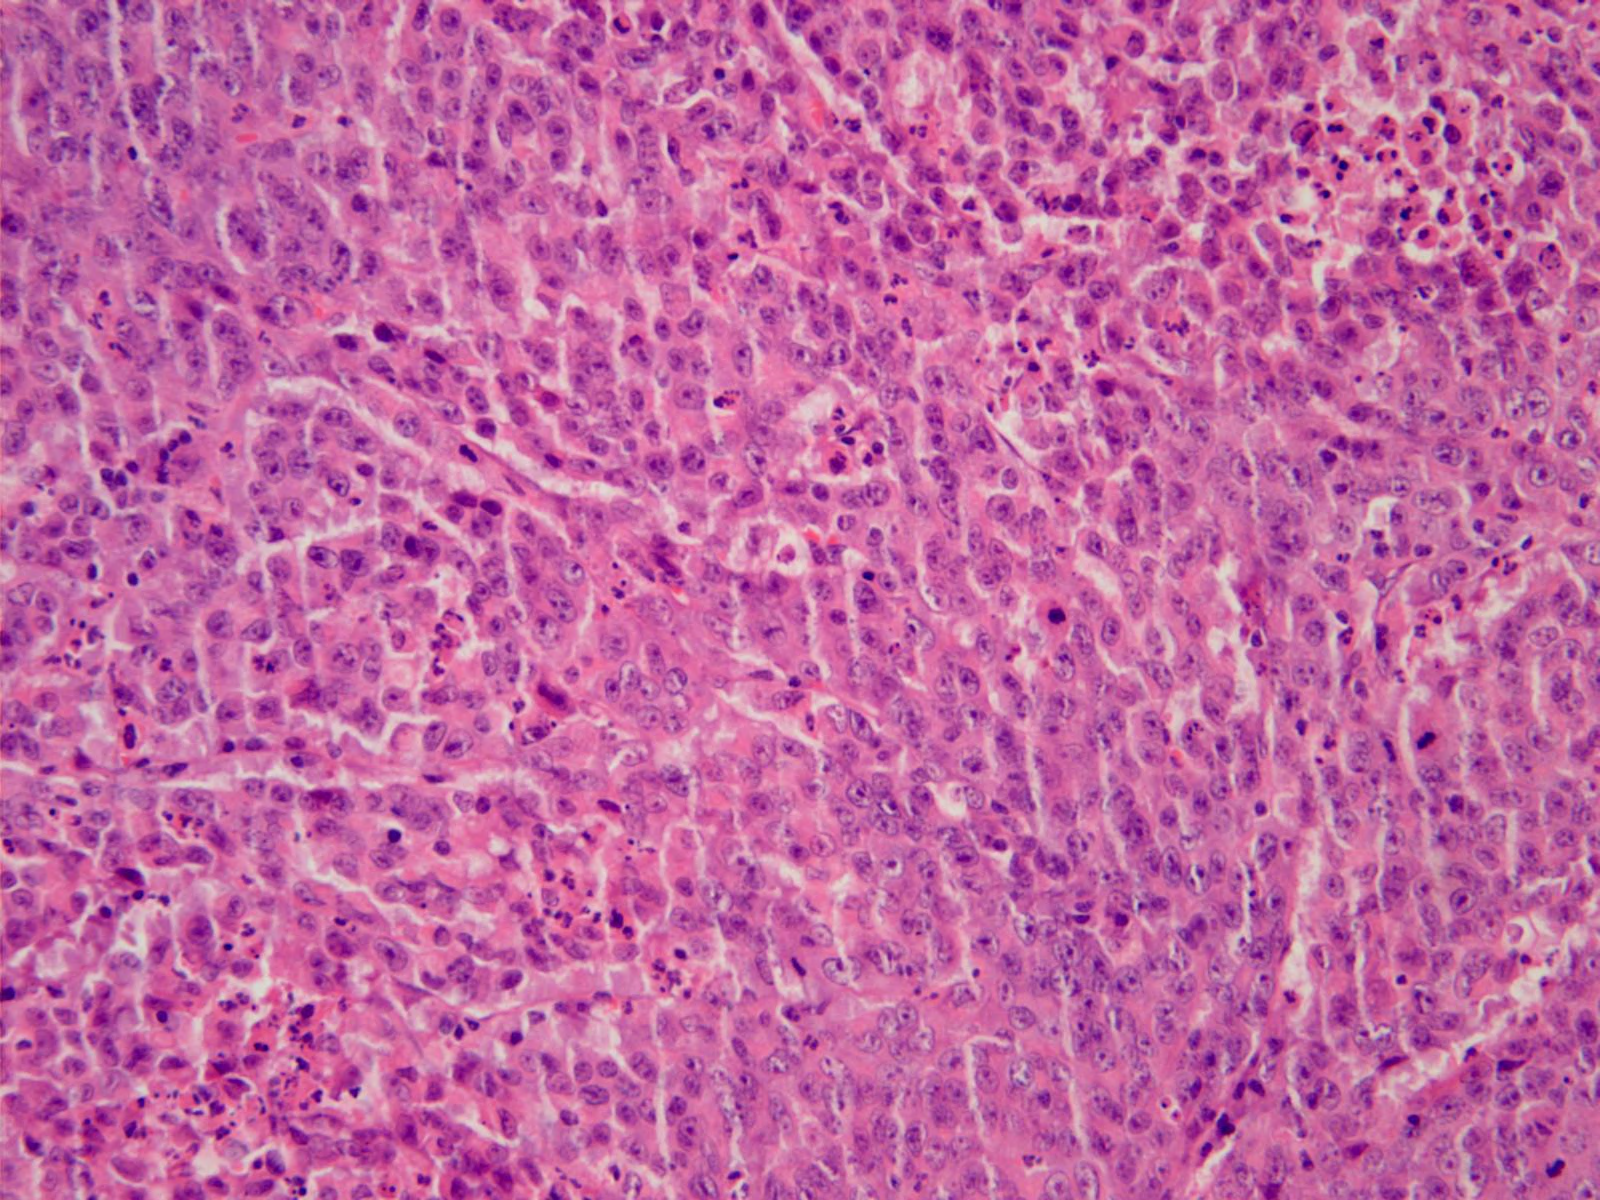
H&E-stained image of one small field of the section, roughly 0.8 x 0.6 mm in extent. Formalin-fixed paraffin-embedded (FFPE) diagnostic section. Stomach, primary tumour sample. Patient: female, age at initial diagnosis 74 years. Histologic grade: G3 (poorly differentiated).
• lymph nodes positive (case pathology): 4 of 8 examined
• diagnosis: Adenocarcinoma, NOS